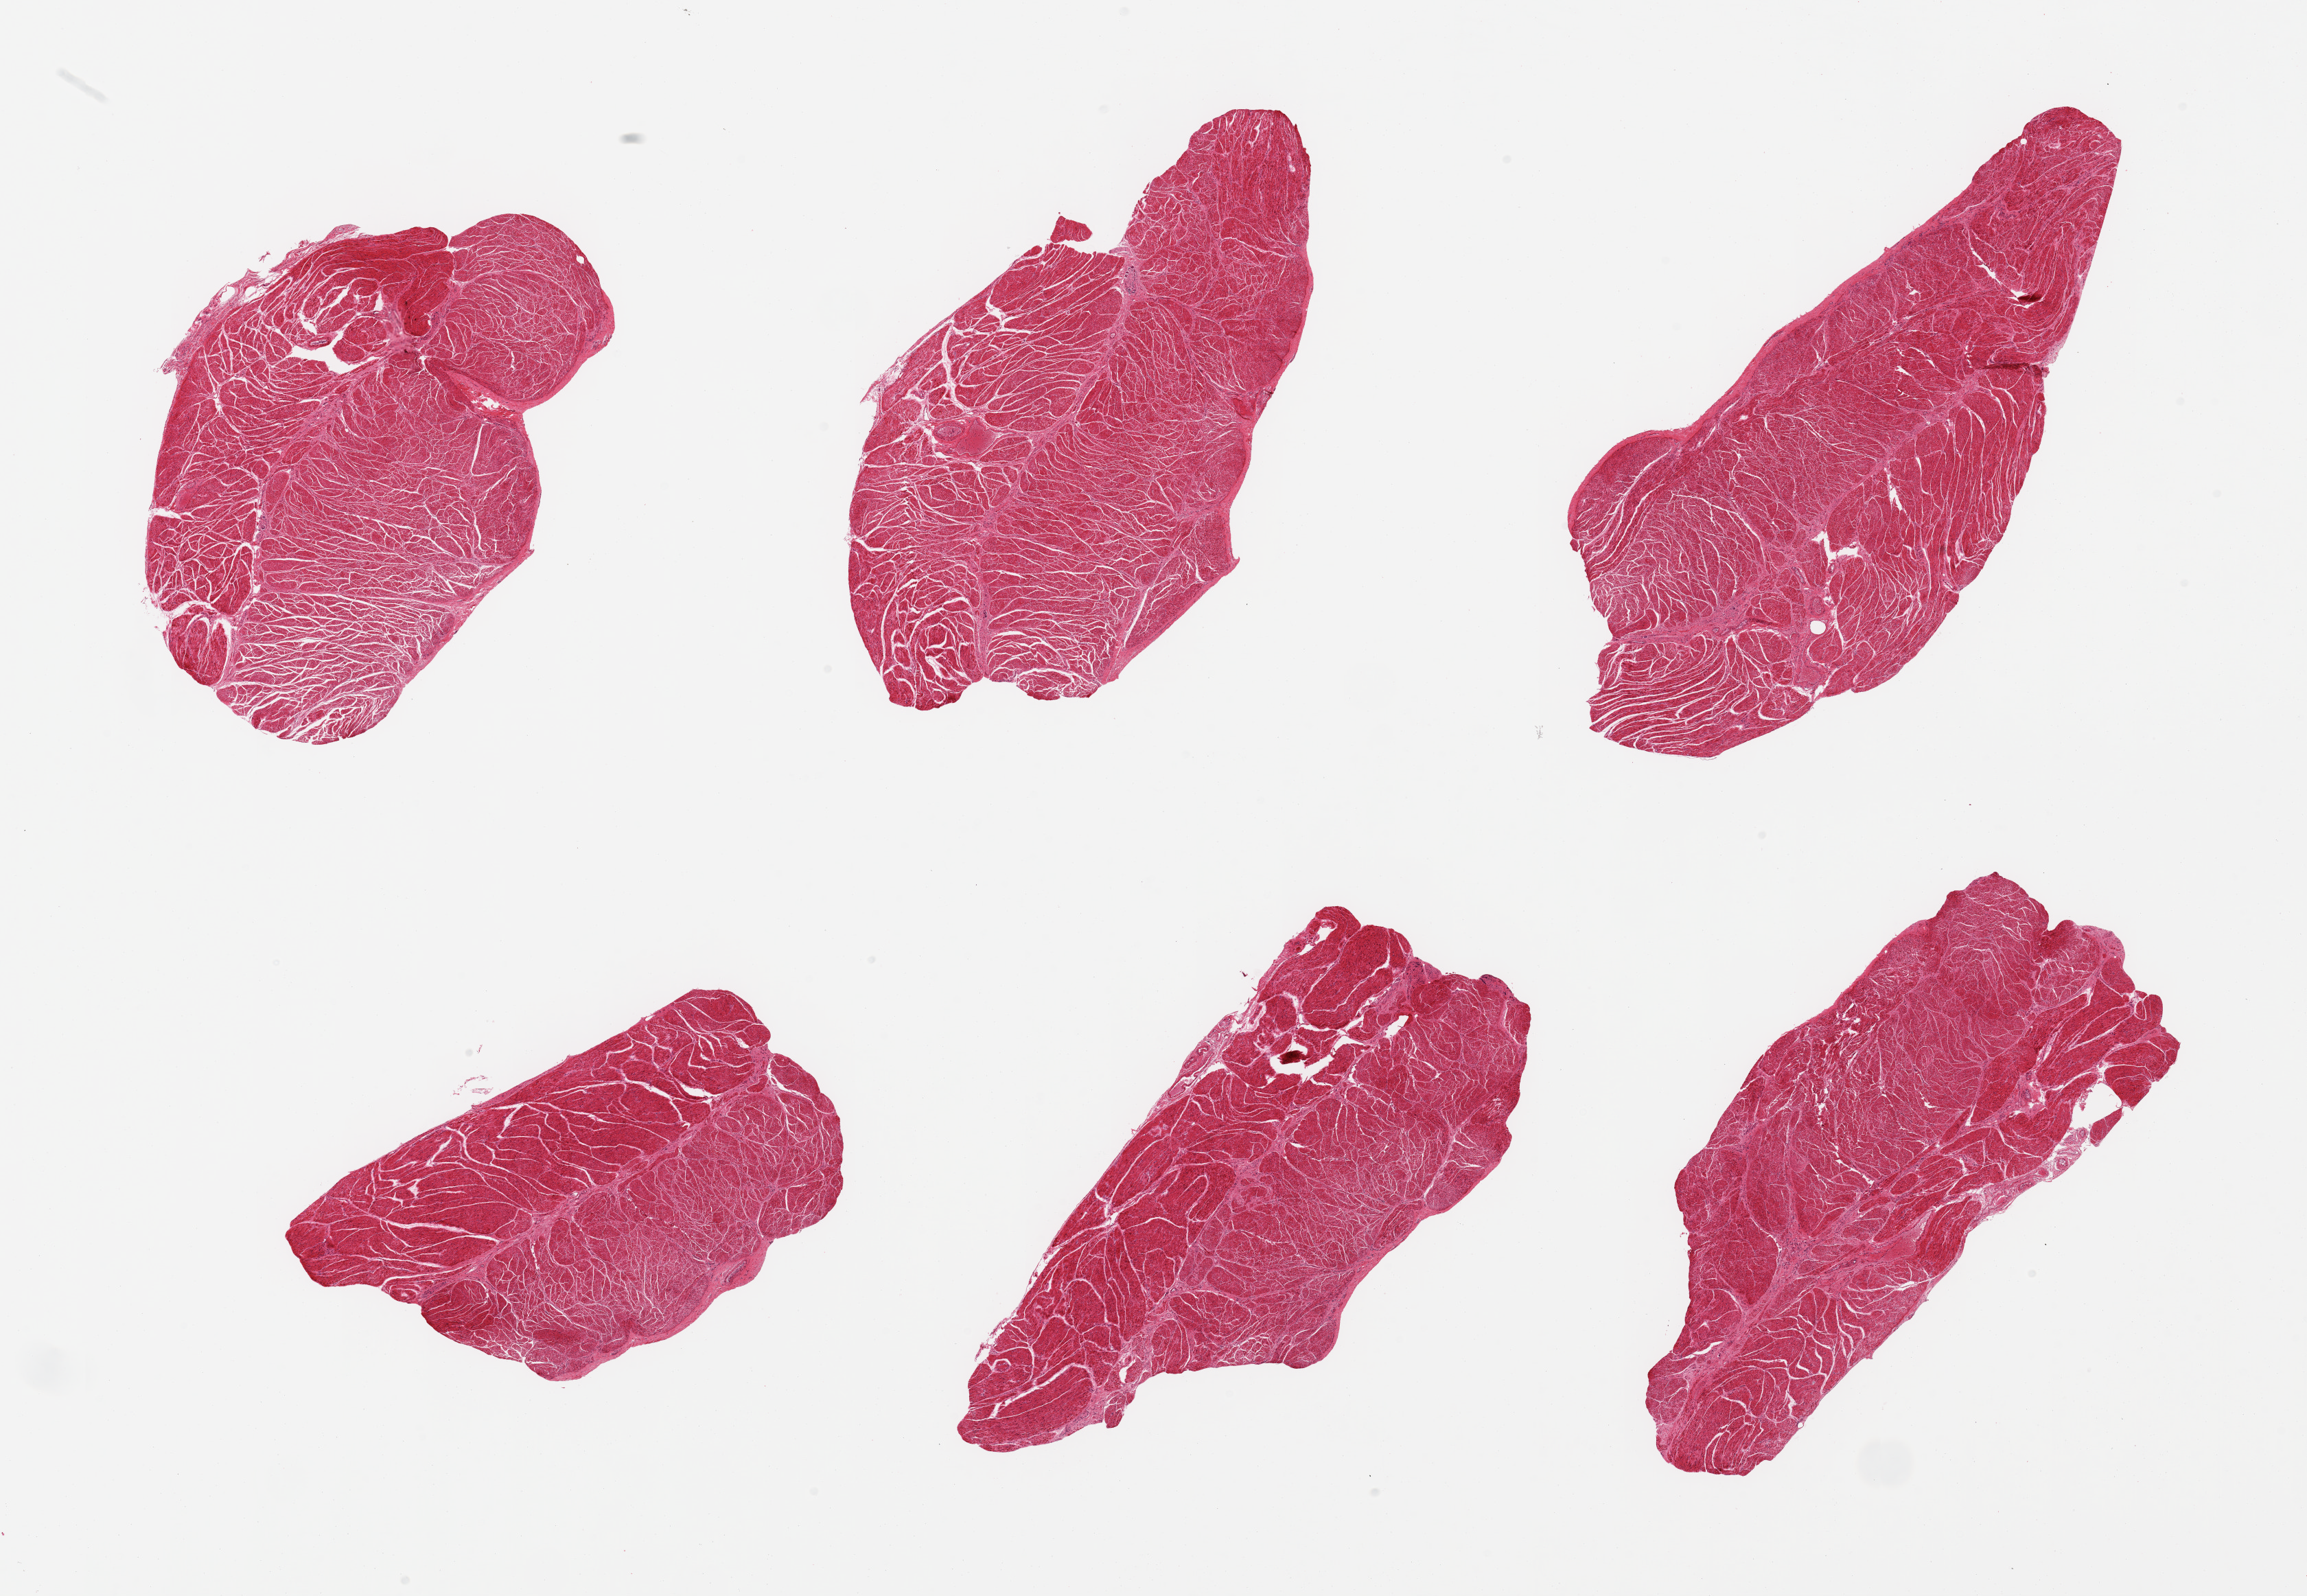
Haematoxylin and eosin whole-slide image — shown as a low-resolution overview of the whole scanned area (about 26.6 x 18.4 mm). PAXgene-fixed paraffin-embedded (PFPE) section. Sampled site (target tissue): gastroesophageal junction. Donor tissue sample. Donor sex: female.
Pathologist's review note for this sample: 6 pieces; well dissected: pure muscle.